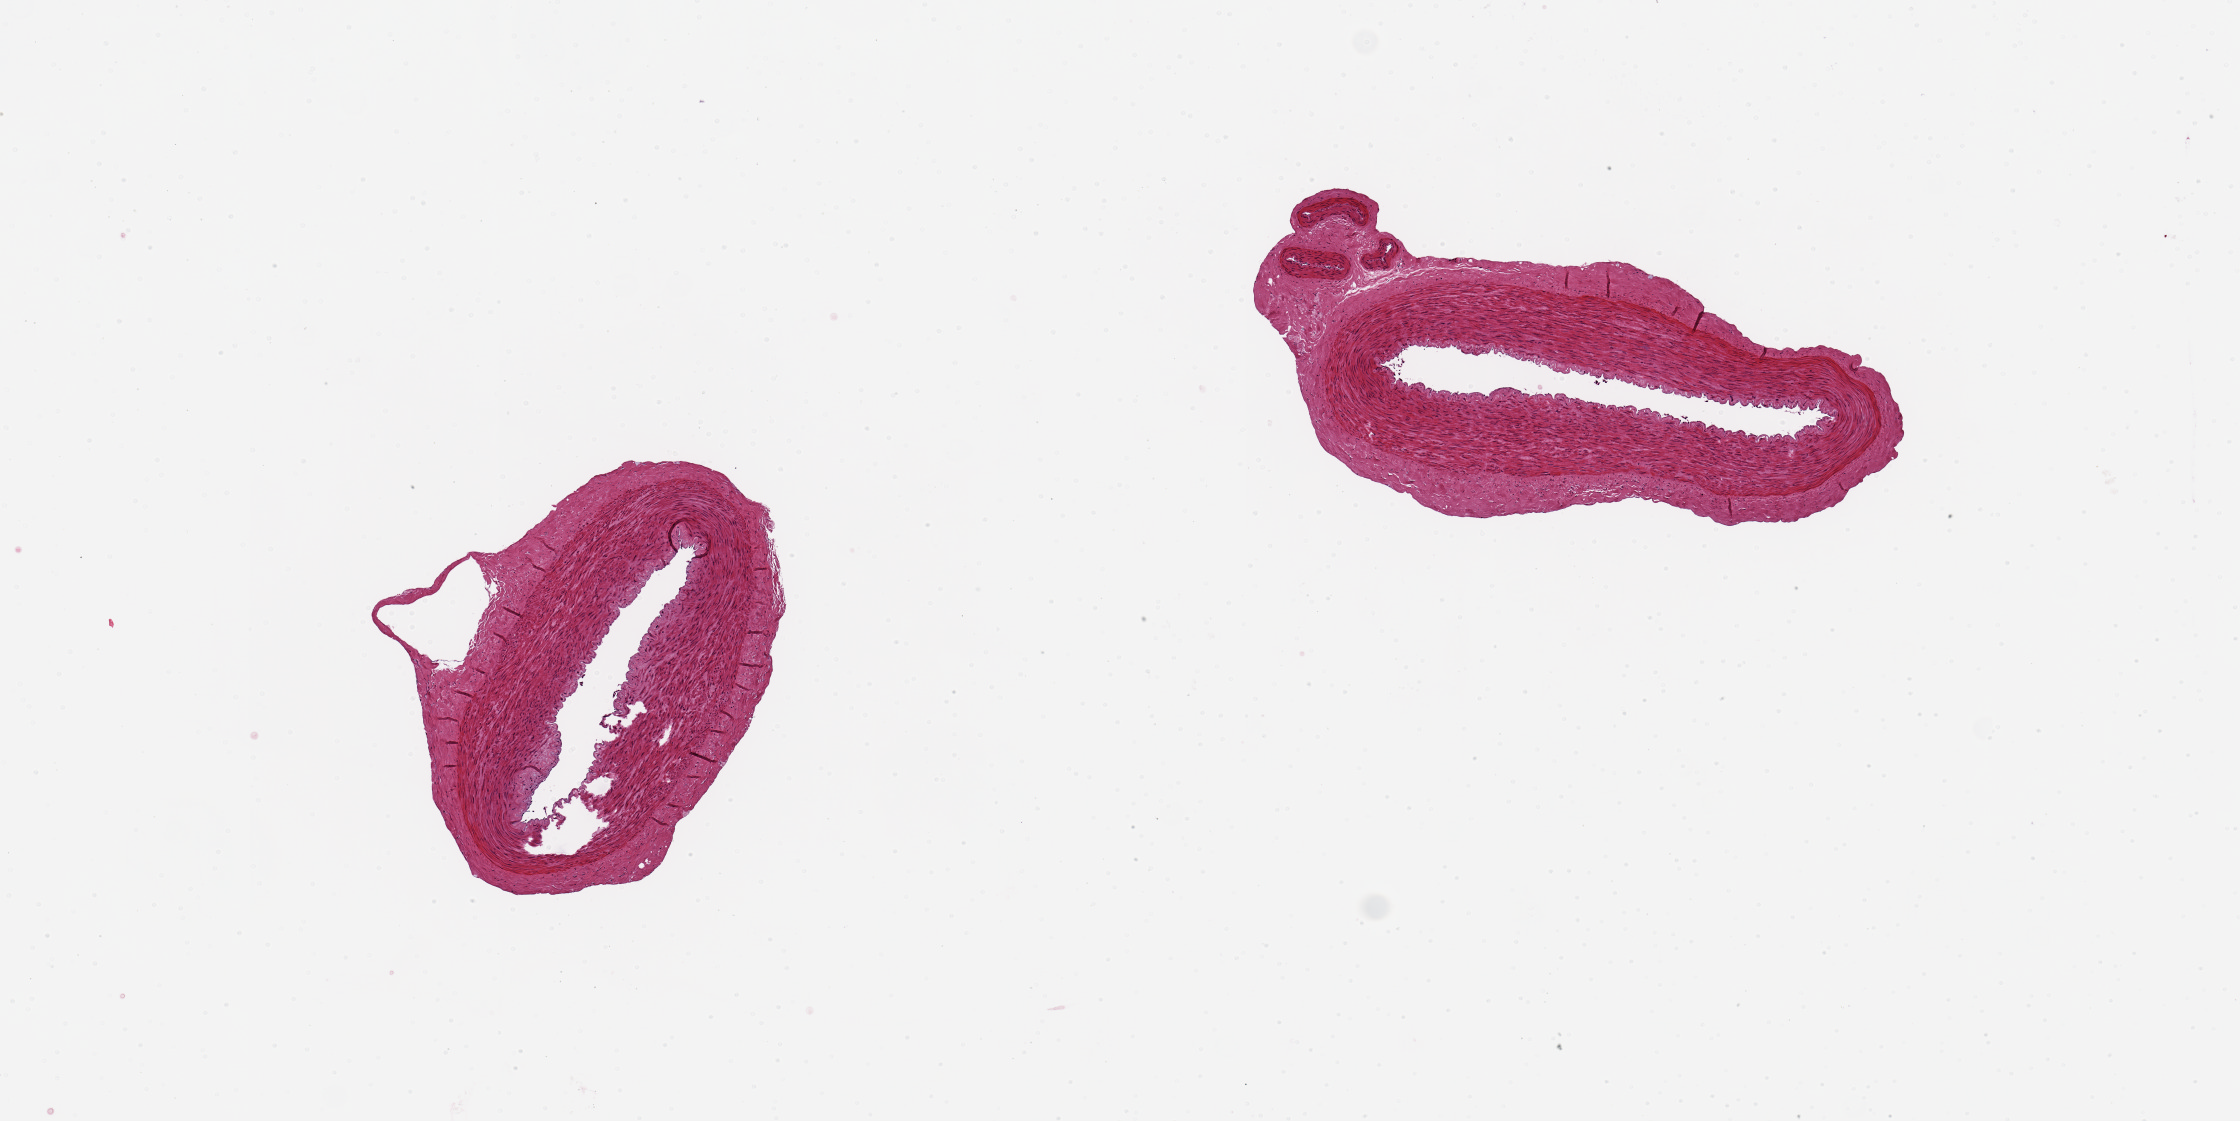
Digitized hematoxylin and eosin (H&E)-stained section, brightfield, whole scanned area (about 8.9 x 4.4 mm) shown as a low-resolution overview, PAXgene-fixed, paraffin-embedded tissue, sampled site (target tissue): tibial artery, donor tissue sample. Donor sex: male.
• reviewer comment on this tissue sample: 2 ~ 2x1mm pieces, relatively clean